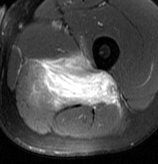
MRI of an extremity soft-tissue mass, one axial slice; position 48 of 70 along the scan axis; T2-weighted fat-saturated; MR volume resampled by the dataset authors to the PET/CT grid (not the native acquisition matrix); 3.27 mm slice thickness; 158 × 164 image matrix, field of view 154 × 160 mm. Male patient. Case-level facts recorded for this patient, not image findings: histological type: extraskeletal osteosarcoma; grade: high; site of the primary tumour: left adductur.
Annotated regions visible in this slice (expert contour drawn on MRI and transferred to this co-registered scan by the dataset authors):
- gross tumour volume (mass): bounding box [x1, y1, x2, y2] px = [29, 51, 119, 111]